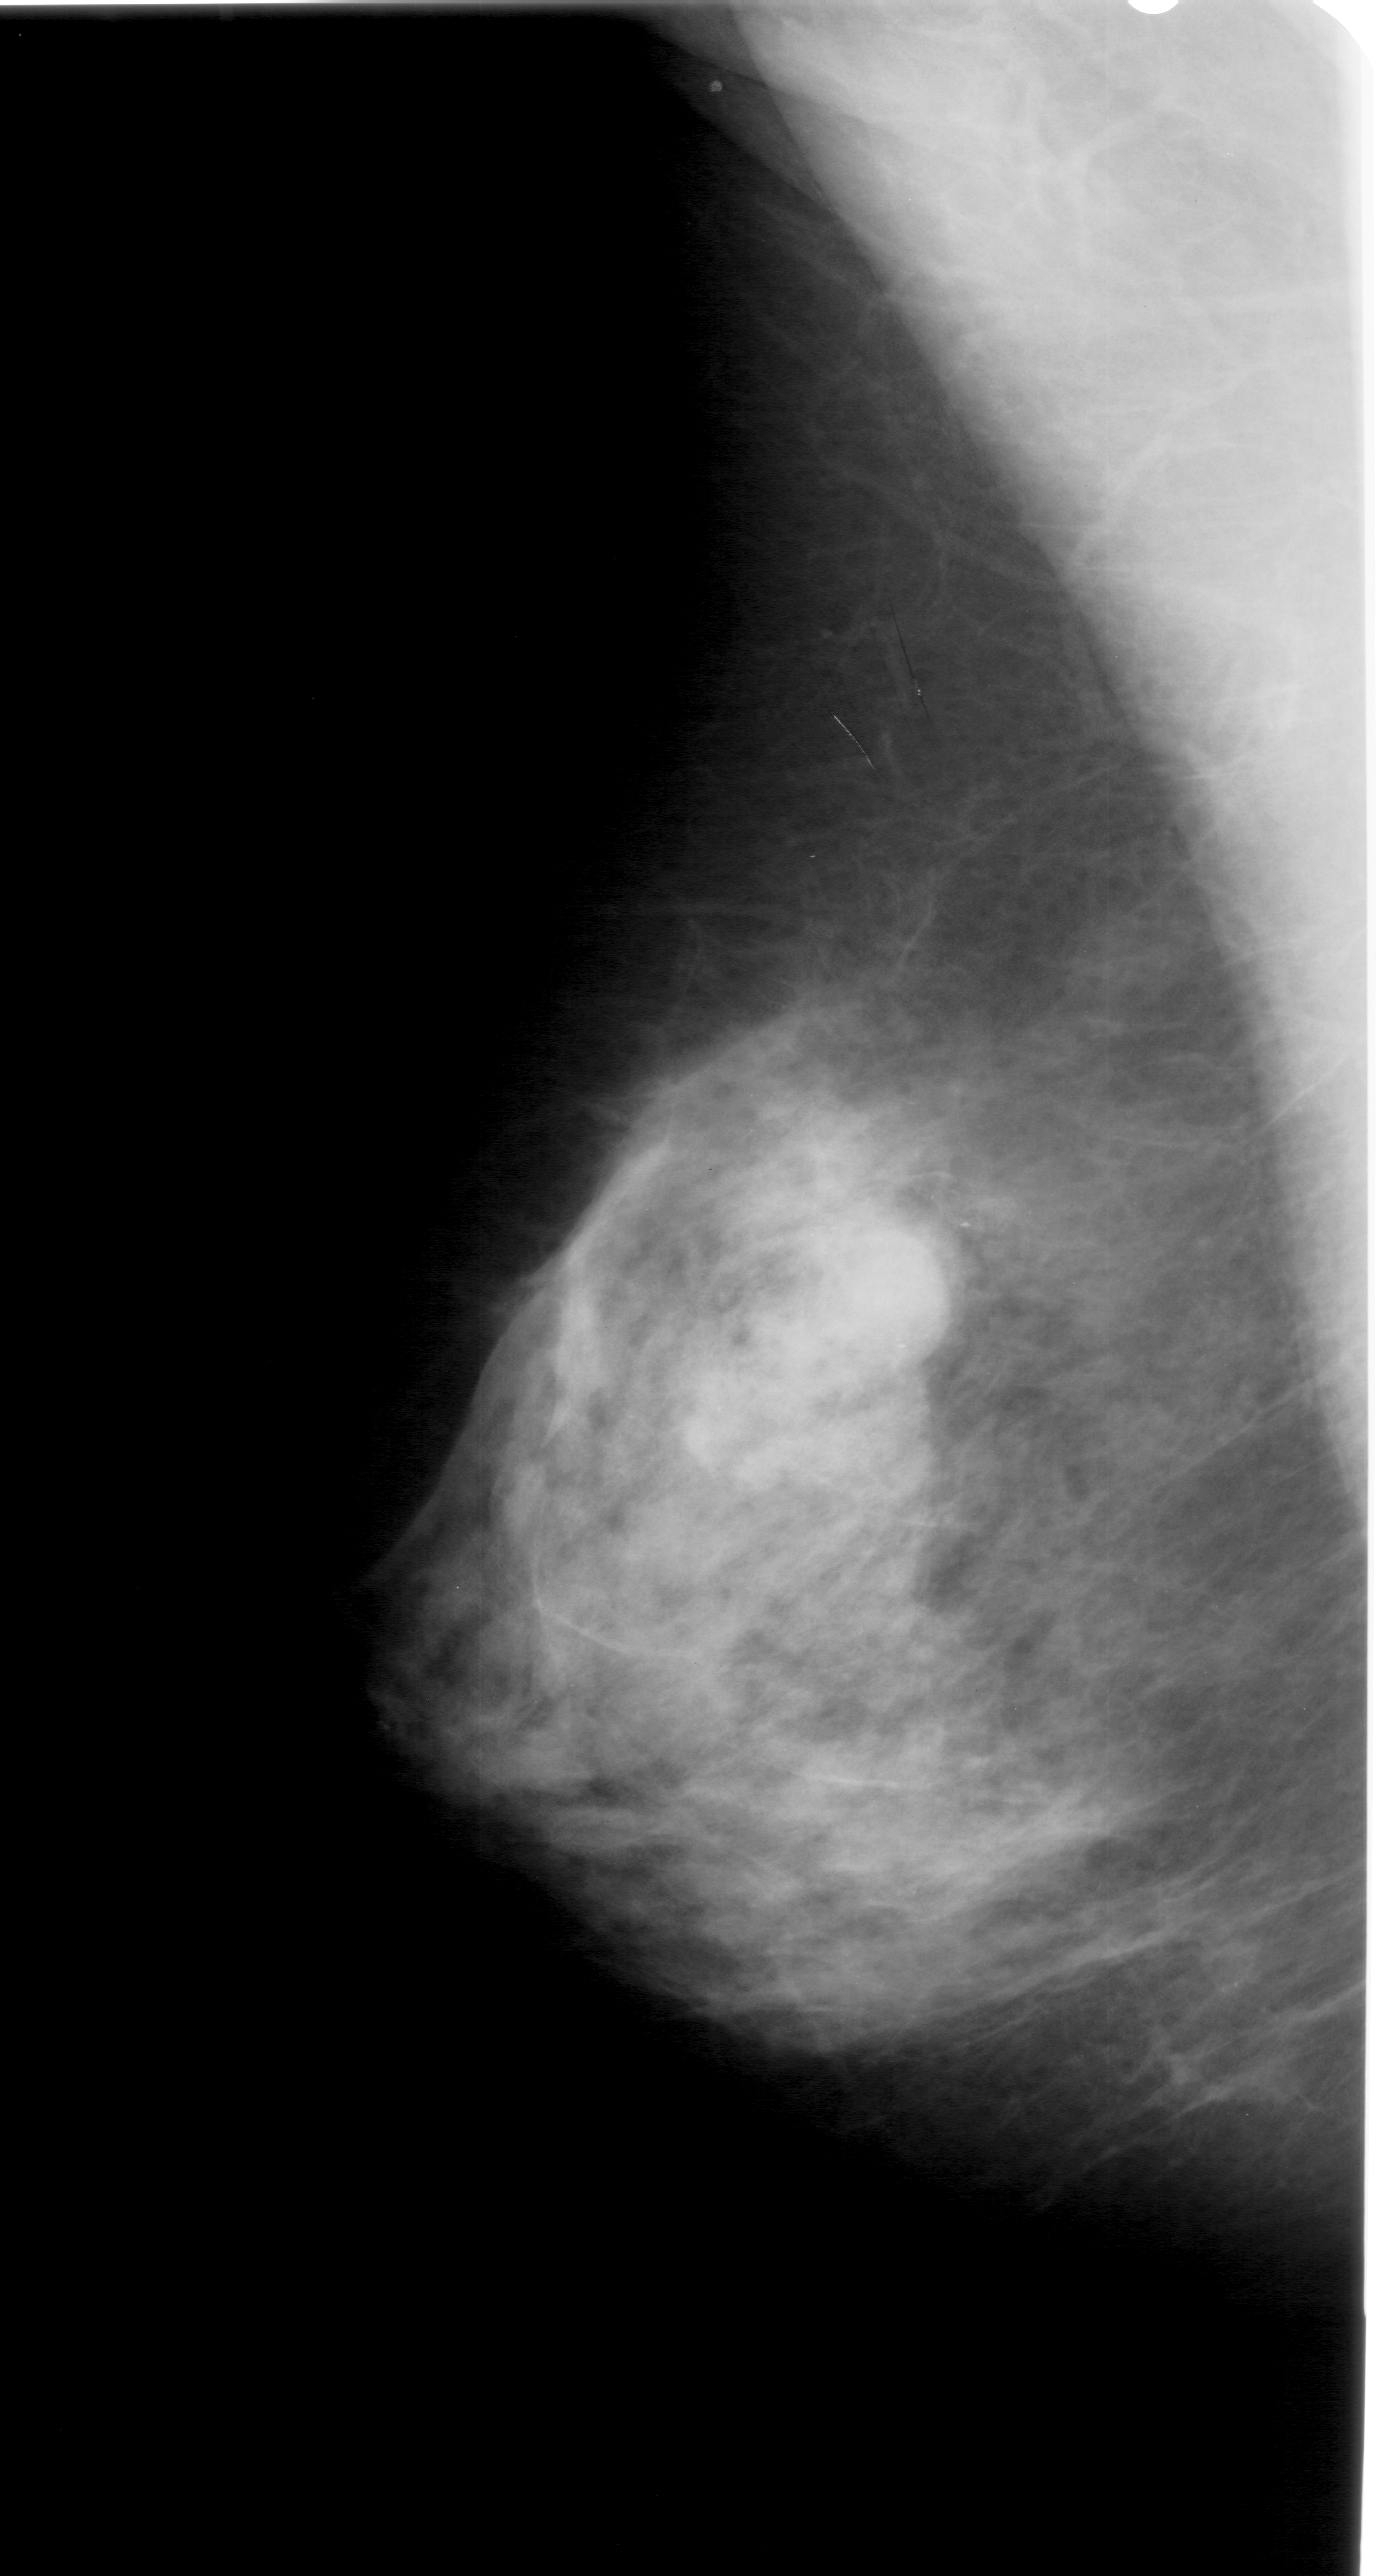
Digitized screen-film mammogram, left breast, mediolateral oblique (MLO) view.
- Marked findings (only marked abnormalities are described; nothing is implied about the rest of the image): mass, shape round, margins obscured; BI-RADS assessment category 4; subtlety rating 3 on a 1 (subtle) to 5 (obvious) scale; pathology (as recorded): benign.